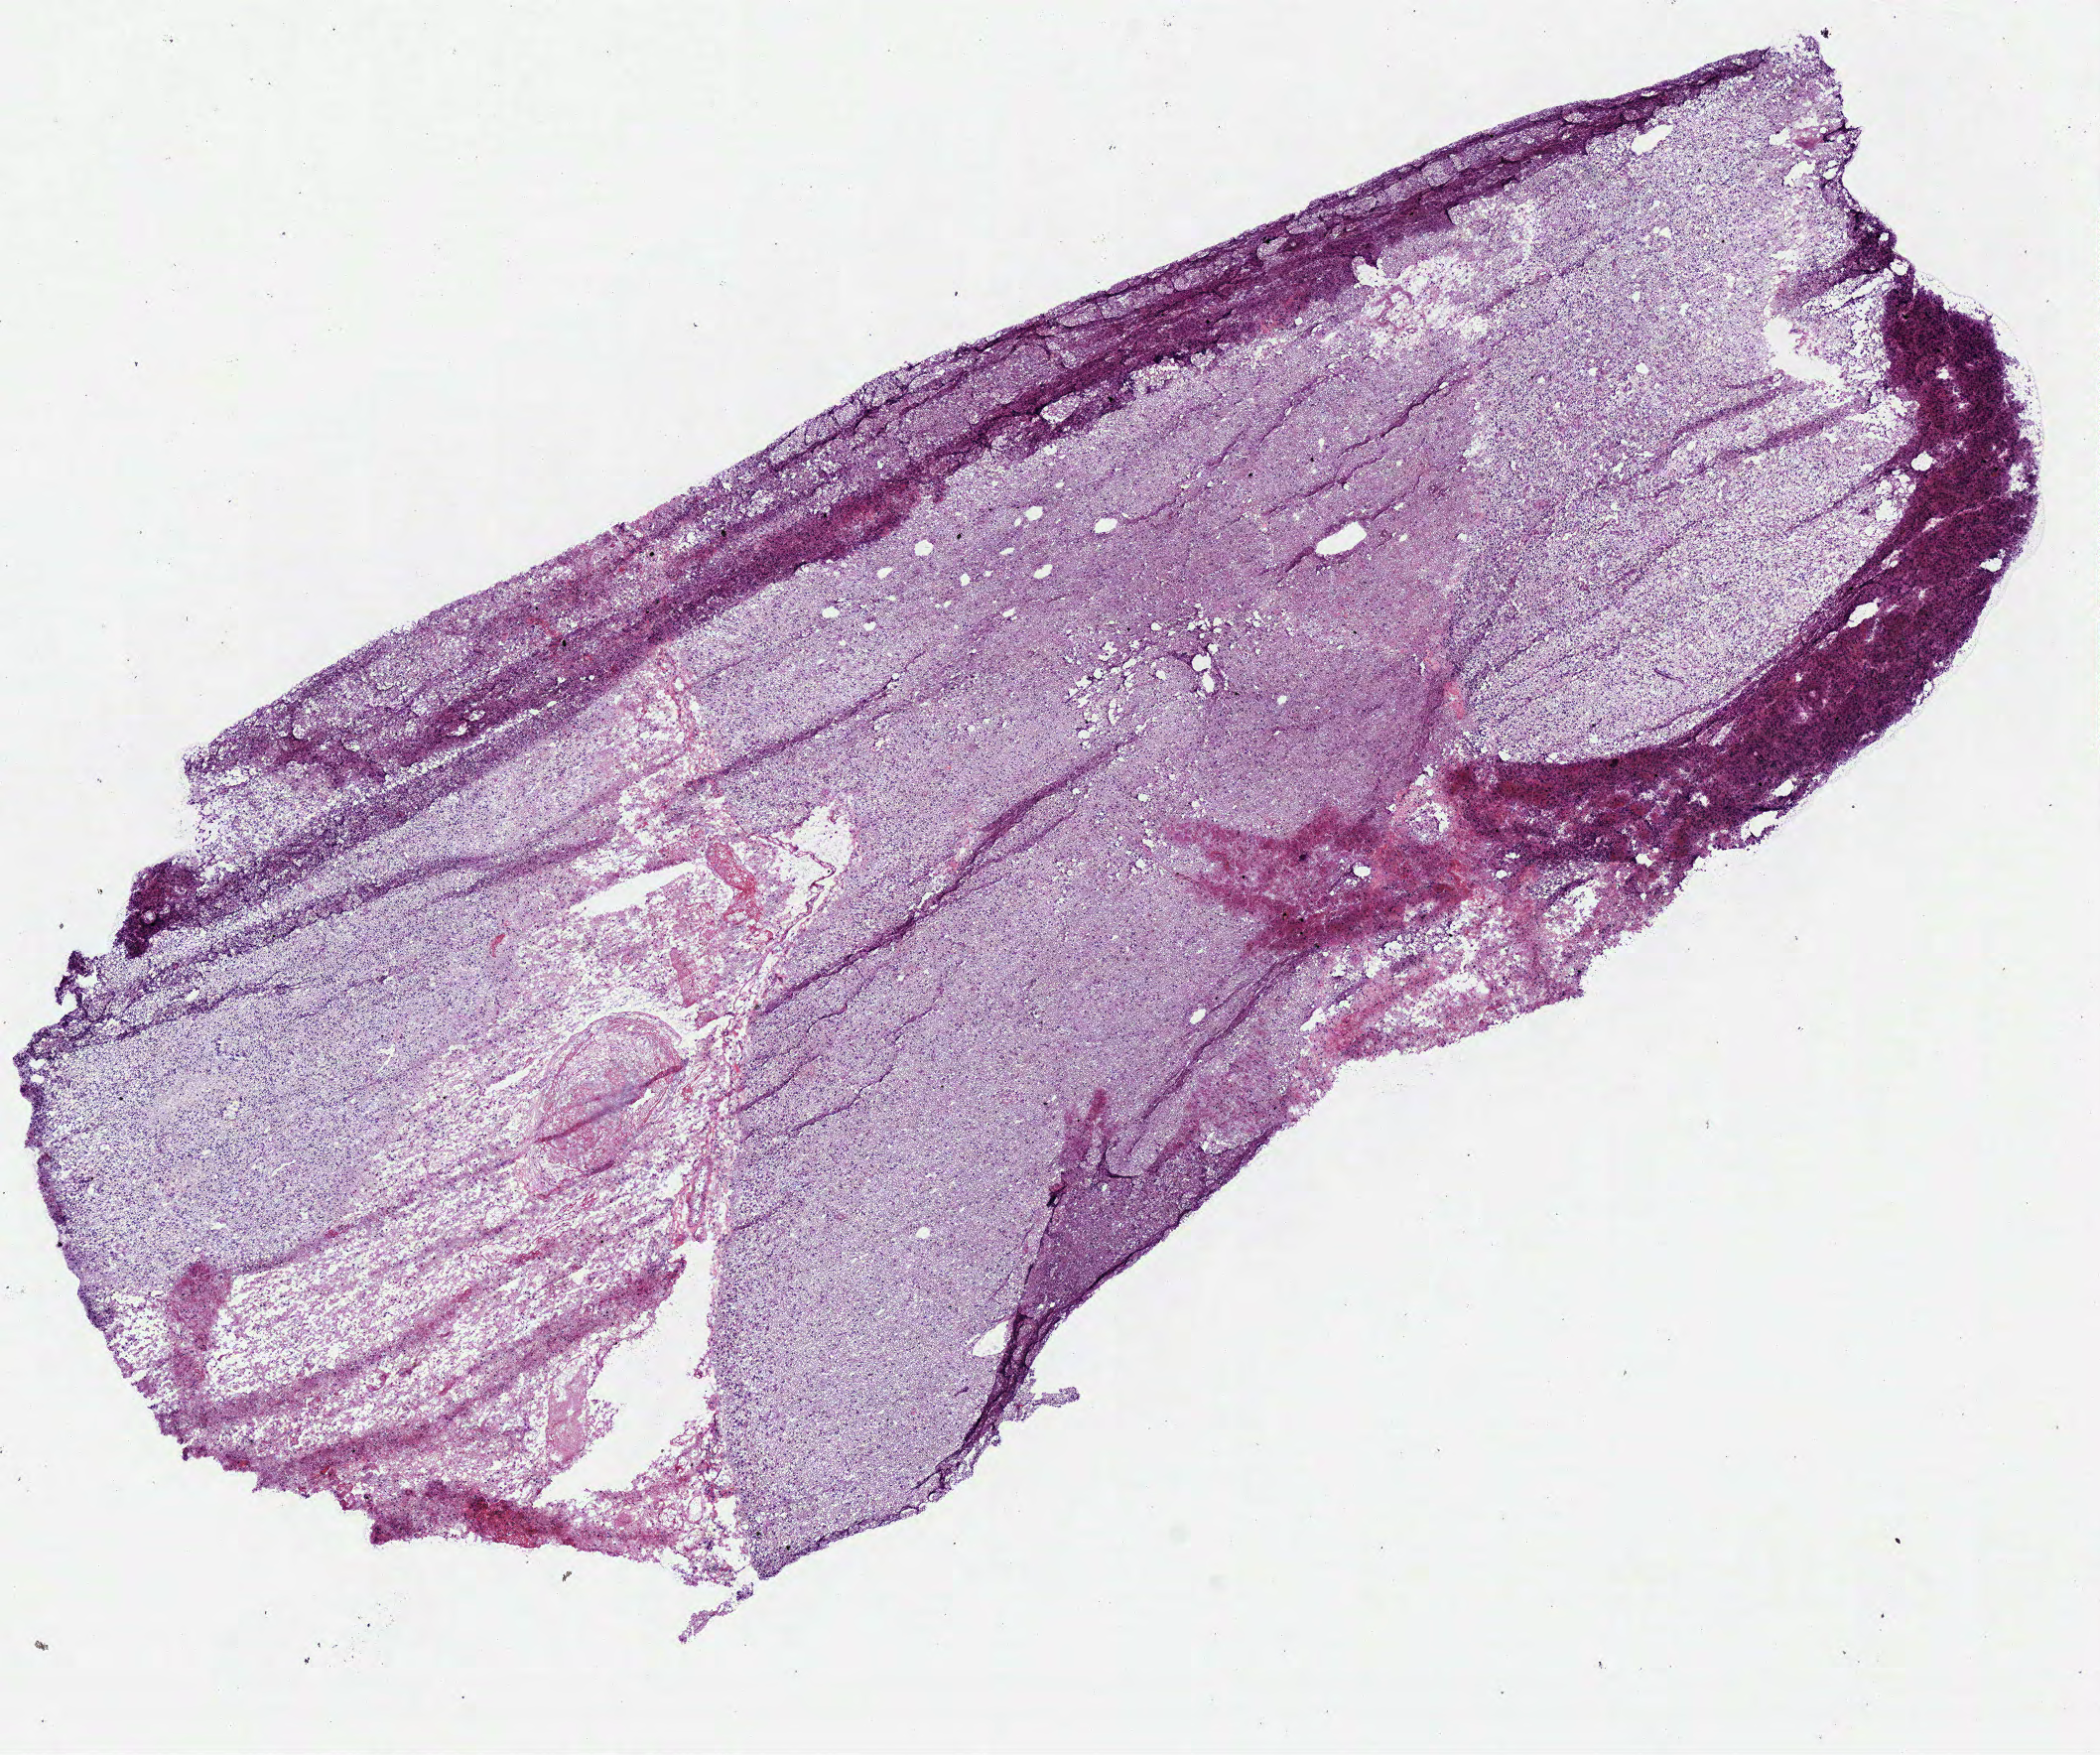
Digitized Hematoxylin and eosin (H&E) stained tissue section (whole slide), whole scanned area (about 8.3 x 7.0 mm) shown as a low-resolution overview, frozen section from the bottom of the tissue portion, primary tumour sample from the brain. Patient: female, age at initial diagnosis 64 years. Slide review estimates, as recorded: tumour cells 85%, tumour nuclei 75%.
Diagnosis: Glioblastoma.